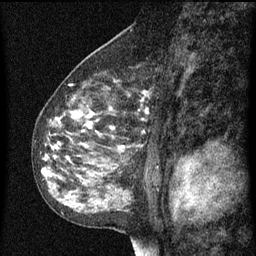
Breast MRI (dynamic contrast-enhanced), one sagittal slice. Position 43 of 60 along the scan axis. Dynamic contrast-enhanced series, image 2 of 3 at this slice position (ordered by acquisition). 1.5 T. TE 4.2 ms, TR 8 ms. 2 mm slice thickness. 256 × 256 image matrix, field of view 180 × 180 mm. Patient: female, 55 years.
Structures marked on this image (semi-automatically segmented with operator editing):
- analysis volume of interest (the breast-tissue region the enhancement analysis was run in; not a lesion): bounding box <34,68,153,151> (left, top, right, bottom; pixels)
- tumour enhancement mask (voxels above the 70 % enhancement threshold inside the analysis volume of interest): <48,92,149,149>